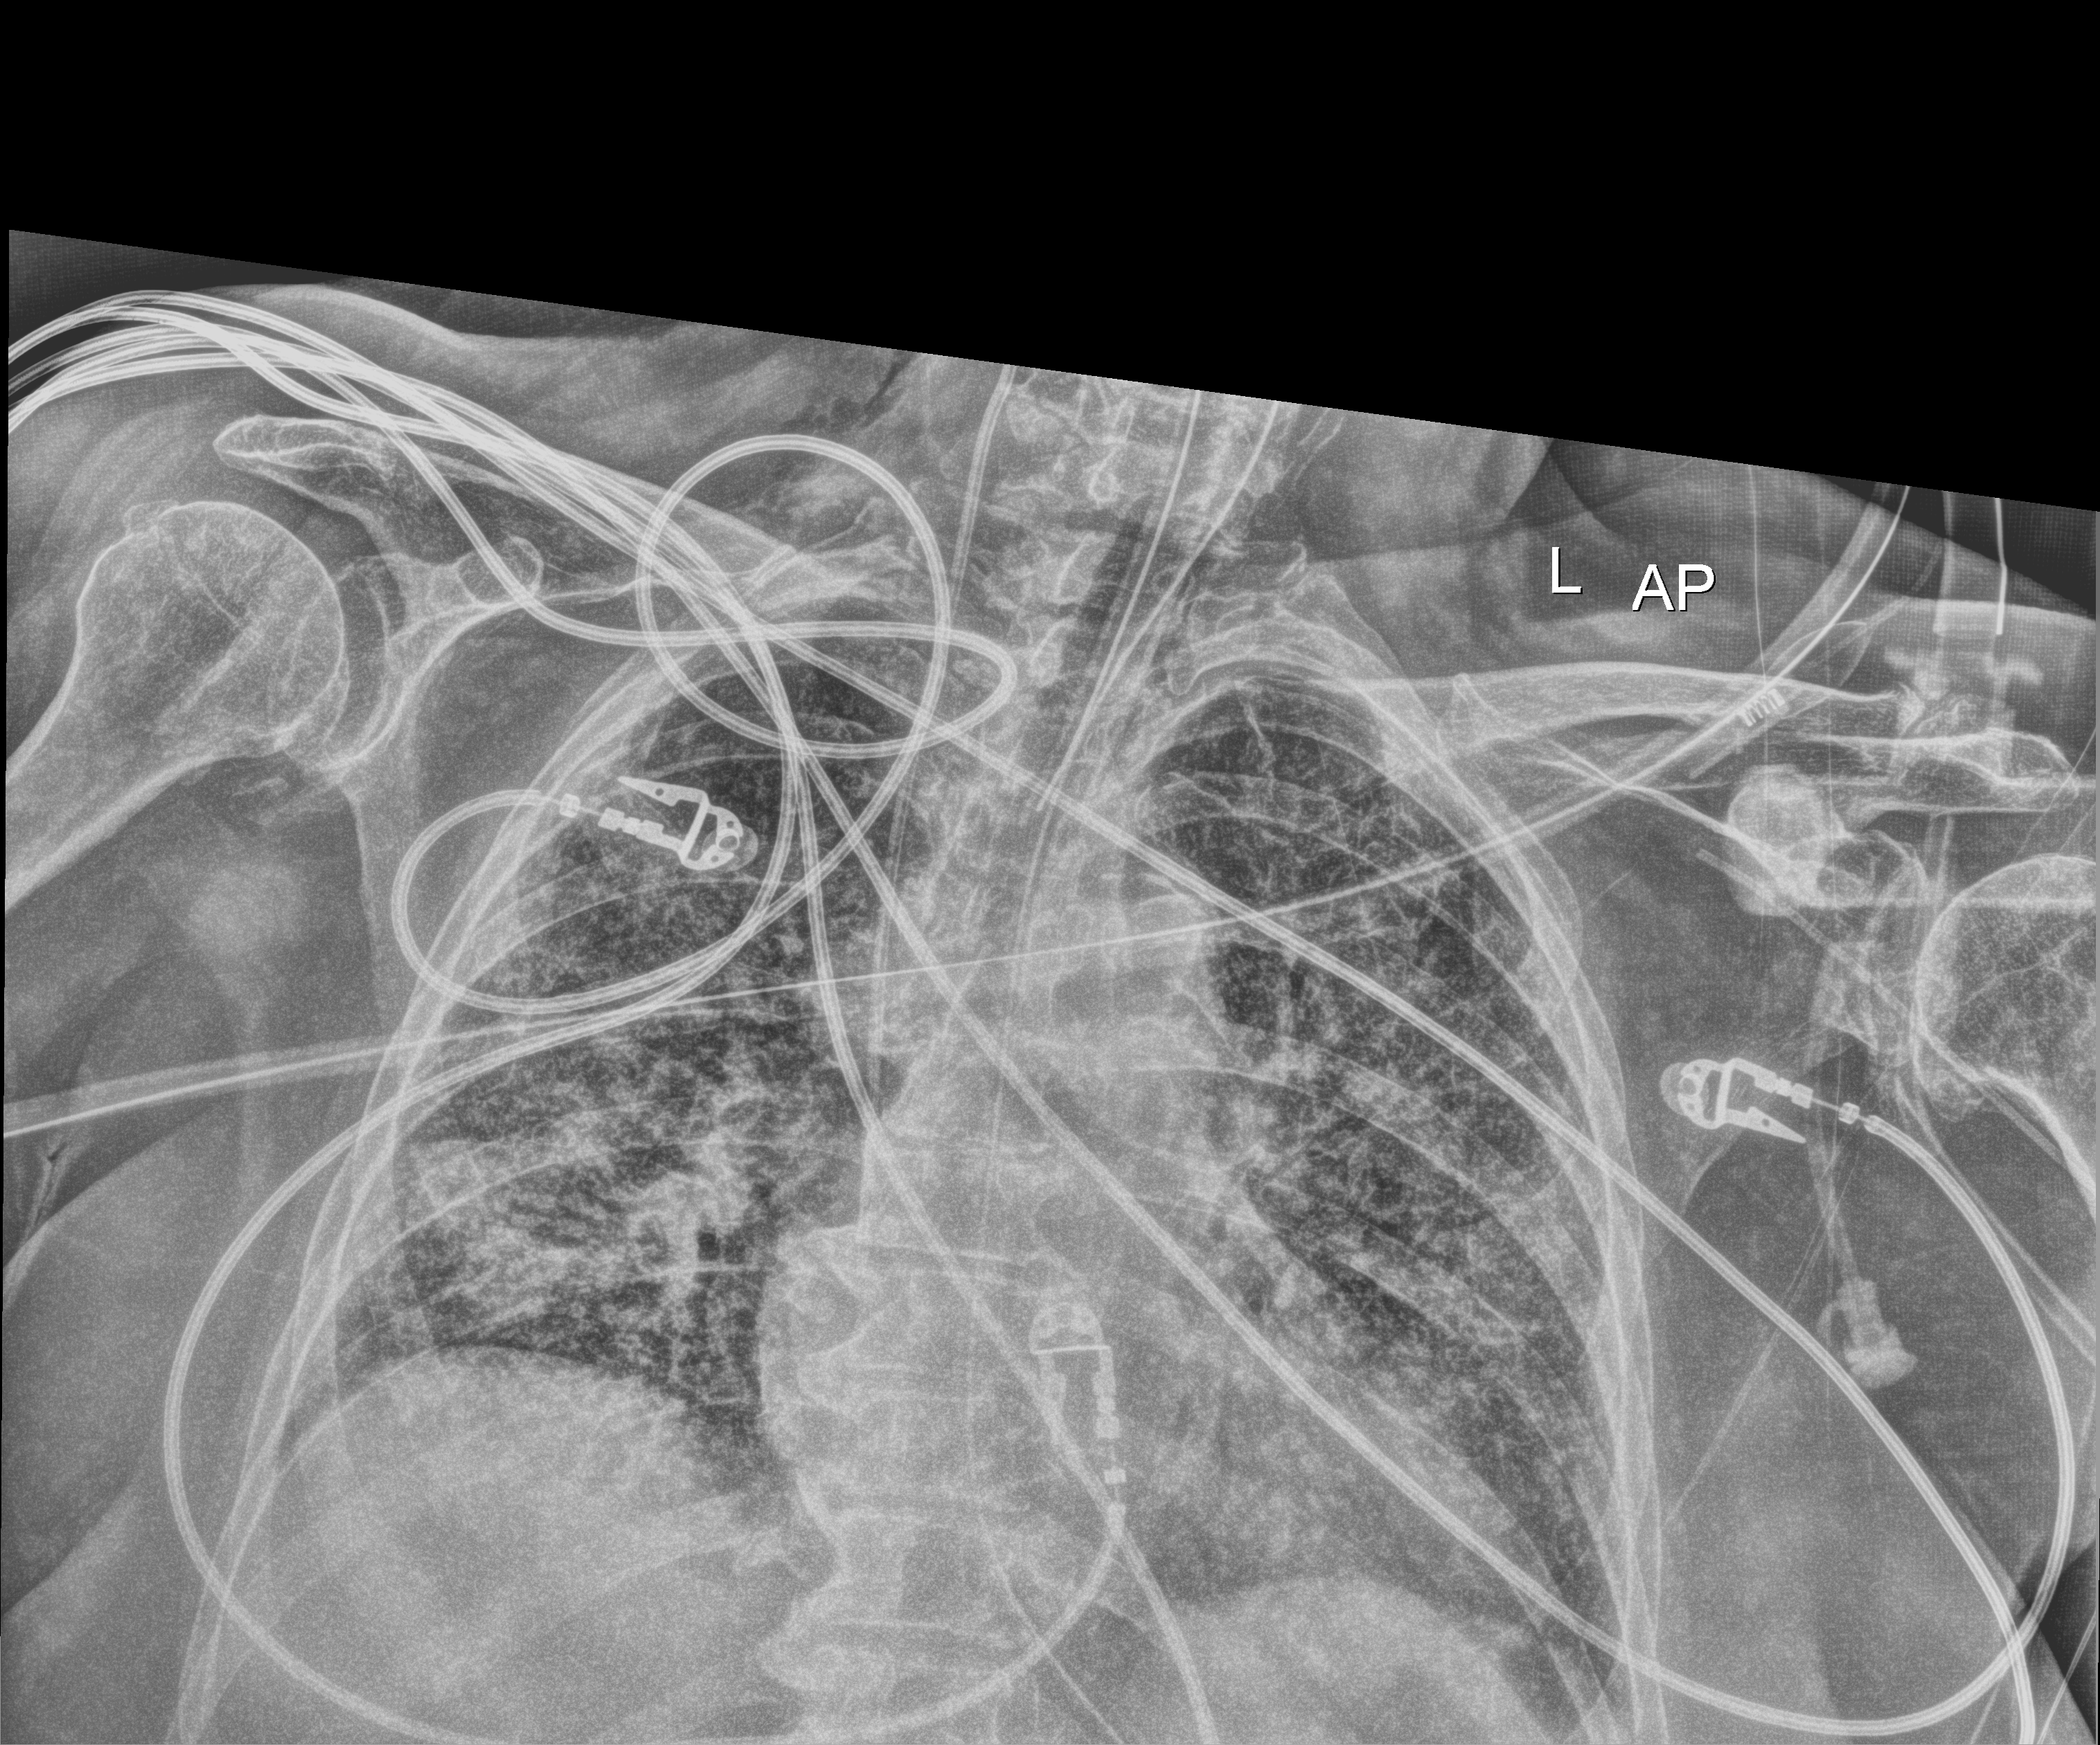
Bedside chest radiograph (digital radiography), anteroposterior (AP) projection. Patient hospitalised with COVID-19; female, aged 75–90 years.
Hospital-stay facts (about this admission, not read from this image; timing relative to this image not recorded):
- chronic kidney disease (admission record): no